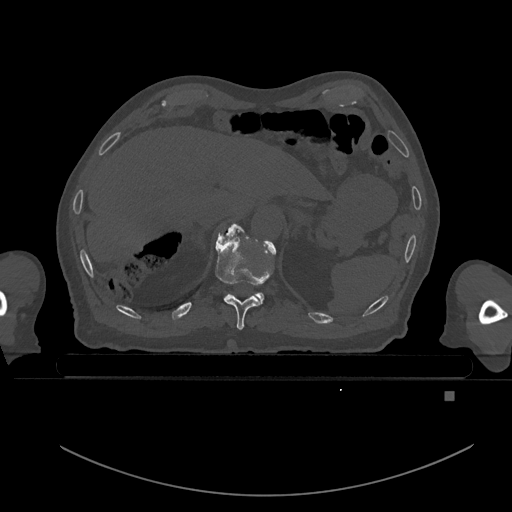
CT including the spine, one axial slice; position 71 of 969 along the scan axis; bone window (W 1800 / L 400 HU); 0.5 mm slice thickness; 512 × 512 image matrix. Male patient, age 82 years. Case-level facts recorded for this patient, not image findings: primary cancer: prostate; vertebrae with lytic lesions (as recorded): T11, T9, T8, T2.
Annotated regions visible in this slice (semi-automatic segmentation, software-assisted and operator-edited):
- T10 vertebra: bounding box [x1, y1, x2, y2] px = [215, 224, 273, 330]
- T11 vertebra: [221, 226, 273, 303]